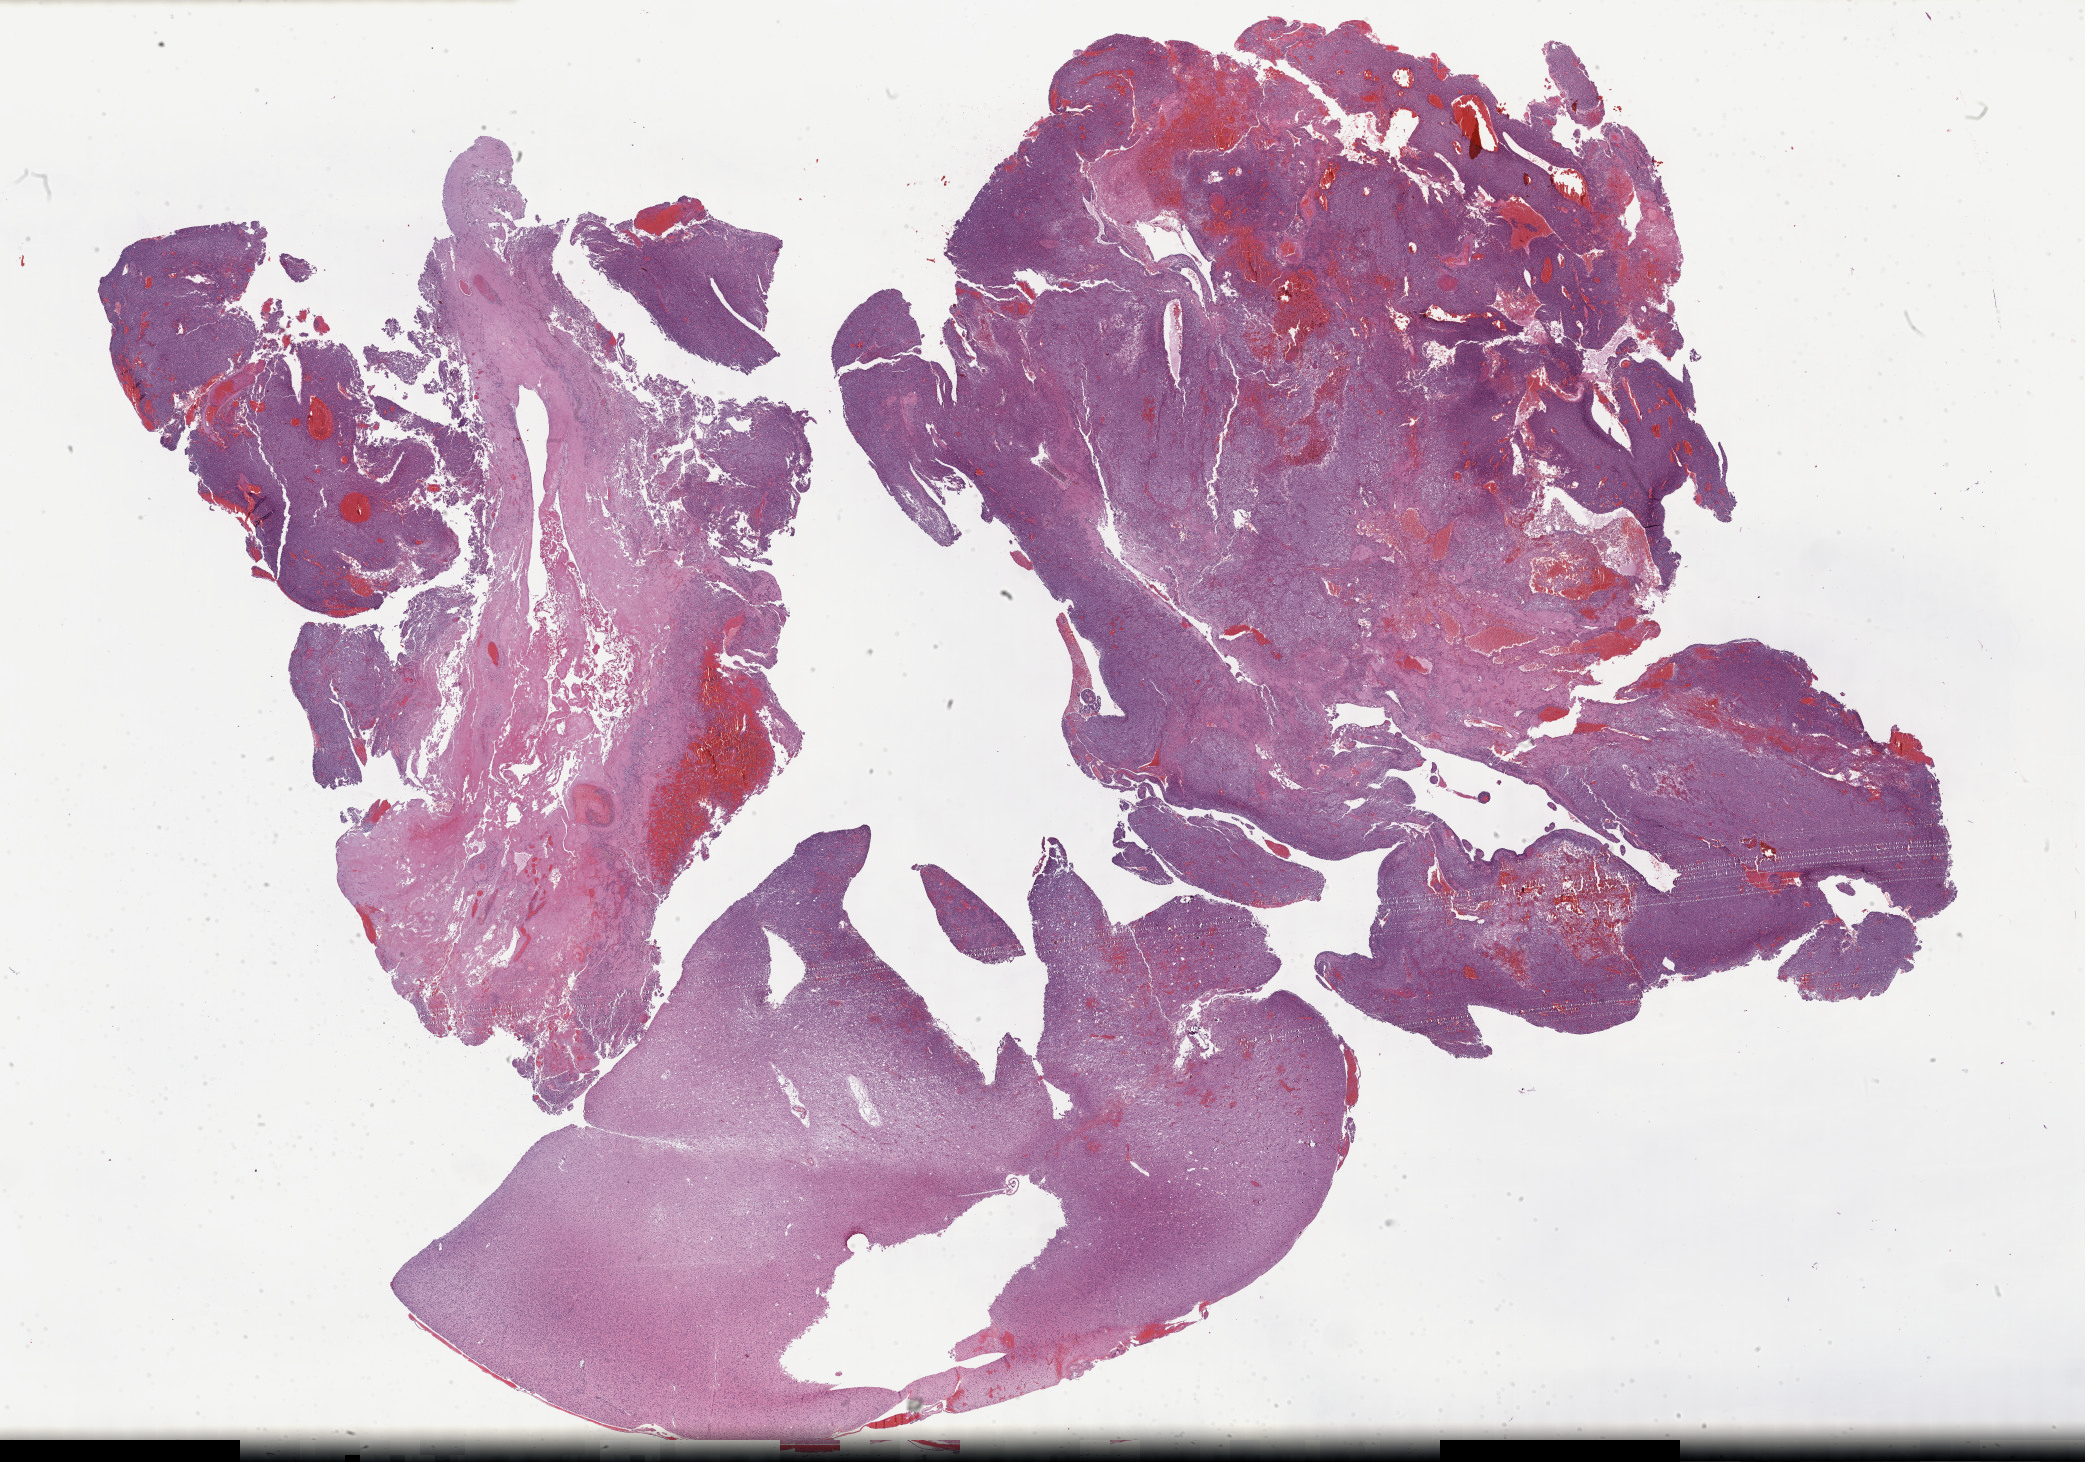
Whole-slide histology image, H&E, whole scanned area (about 33.7 x 23.6 mm, from a 40x scan) shown as a low-resolution overview, formalin-fixed paraffin-embedded (FFPE) diagnostic section, primary tumour sample from the brain. Patient: male, age at initial diagnosis 33 years. Histologic grade: G3 (poorly differentiated).
Diagnosis: Oligodendroglioma, anaplastic (cerebrum).